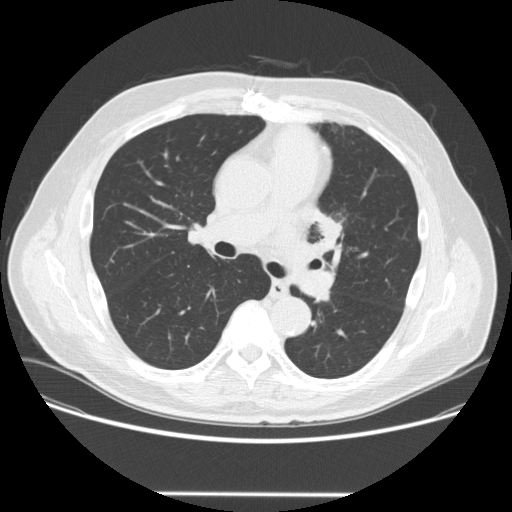
Axial slice from a low-dose chest CT screening exam. Third annual screen. Lung window (W 1500 / L -600 HU). Standard (soft-tissue) reconstruction kernel (STANDARD). 120 kVp. Slice 98 of 253 in the series. 512 × 512 image matrix. Male, age 66 years at enrolment. Former smoker at enrolment.
Lesion marked by an expert reader, bounding box <302,208,354,255> (left, top, right, bottom; pixels). The screening reader recorded 2 non-calcified nodules or masses ≥4 mm on this exam; which of them this box marks is not recorded. Official screen result: positive, other.